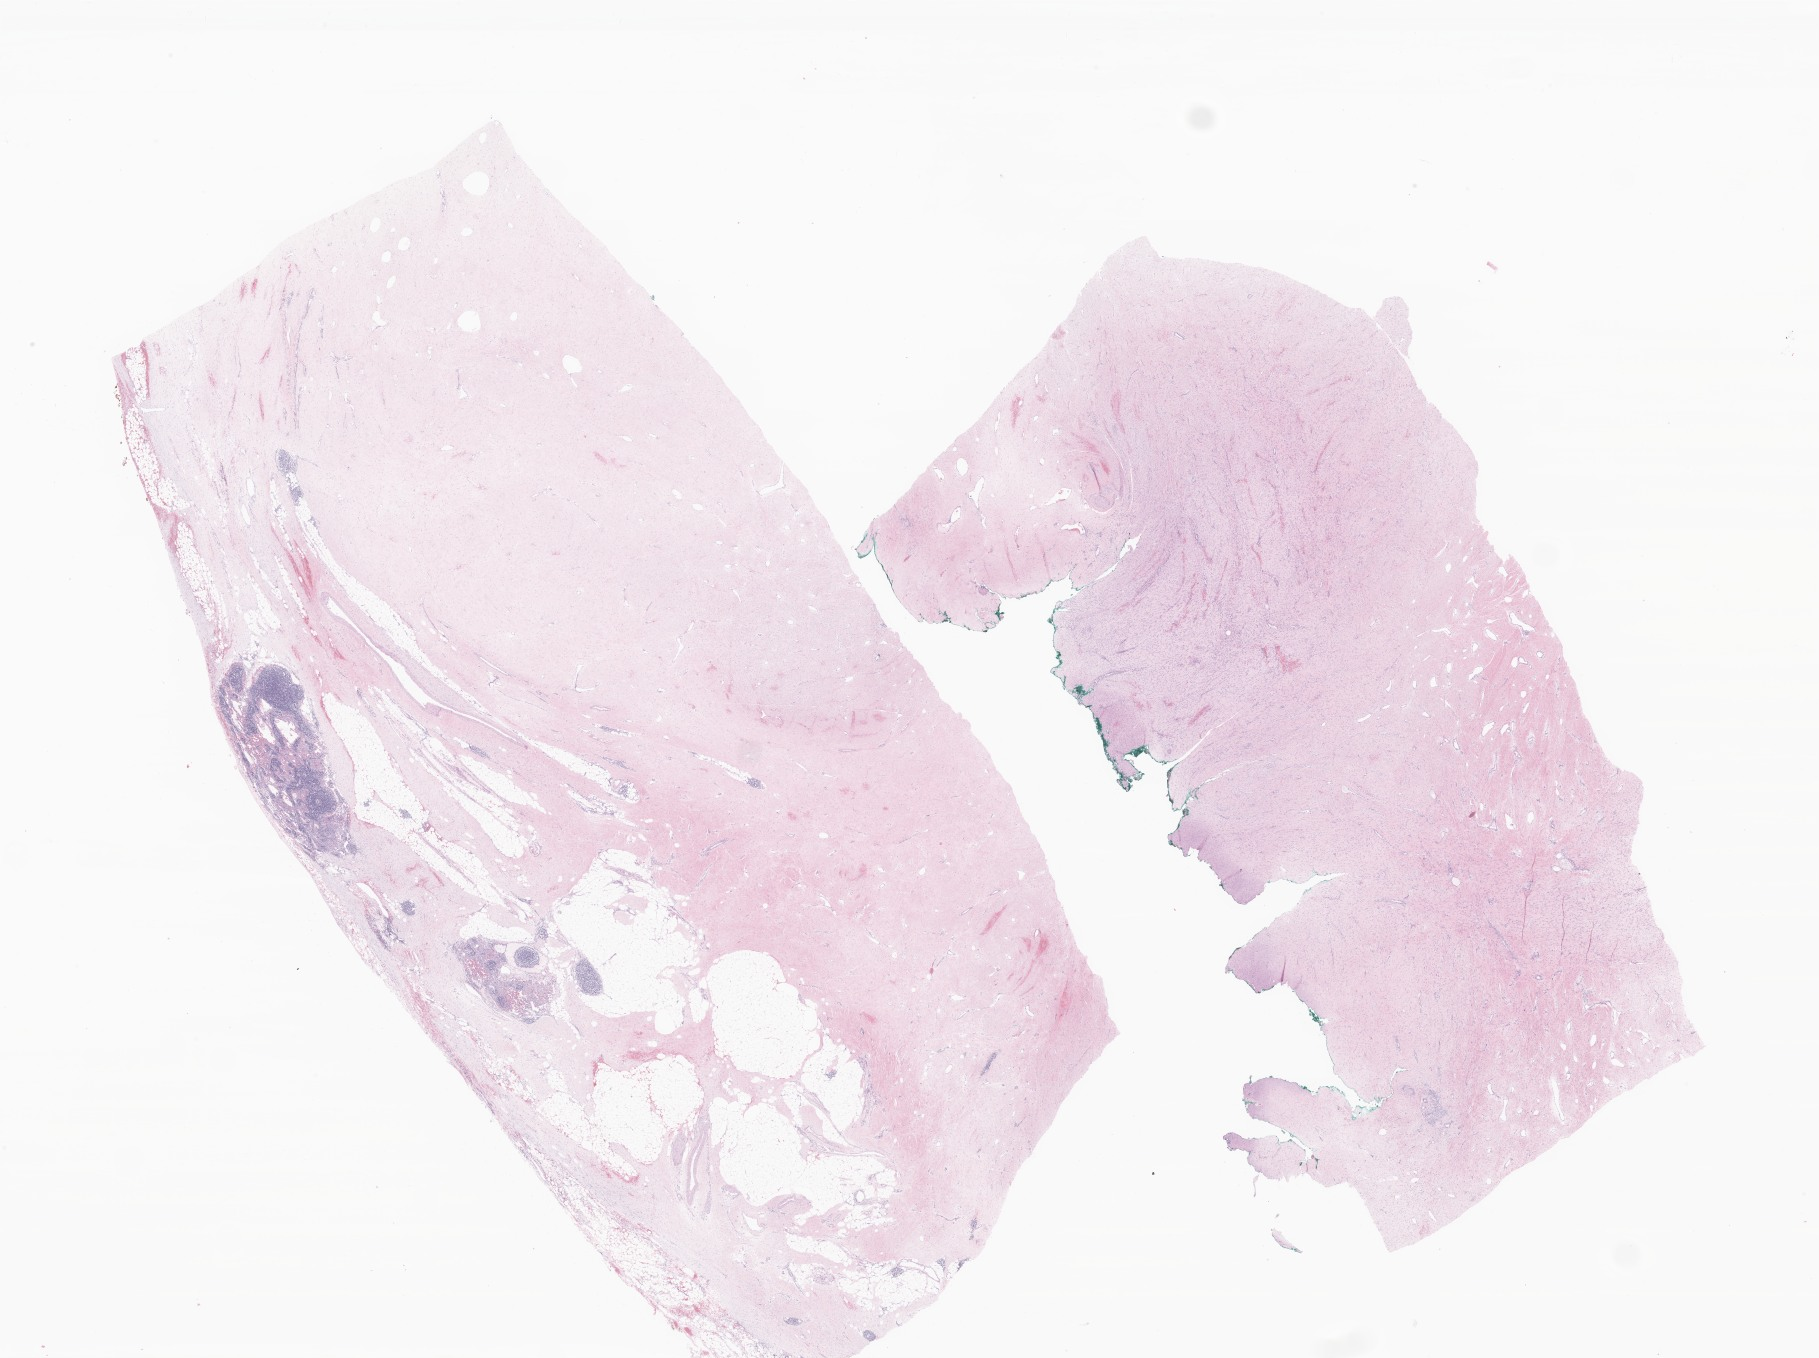
Digitized H&E-stained section of tumor tissue from the abdomen — a low-resolution overview of the entire scanned area, about 30.7 x 22.9 mm. Formalin-fixed paraffin-embedded section. Patient: male, age 214 months.
Diagnosis: Abdominal fibromatosis.